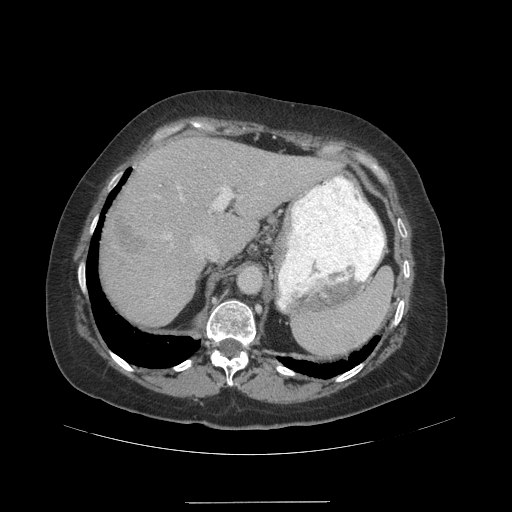
Contrast-enhanced abdominal CT (liver protocol), one axial slice; slice 72 of 99 in the series (ordered by position); reconstruction kernel STANDARD; soft-tissue window (W 400 / L 40 HU); 2.5 mm slice thickness; 512 × 512 image matrix, field of view 440 × 440 mm. Case-level facts recorded for this patient, not image findings: diagnosis: hepatocellular carcinoma (patient treated with transarterial chemoembolisation; whether this scan precedes or follows treatment is not stated here); TNM stage (as recorded): Stage-IVA; Child-Pugh class: A.
Annotated regions visible in this slice (semi-automatically segmented with operator editing):
- abdominal aorta: box from (x=237, y=265) to (x=262, y=293) px
- liver parenchyma outside the tumour (the mass and vessels are separate outlines, so this box may not span the whole liver): (x=102, y=136)–(x=339, y=324)
- mass: (x=109, y=214)–(x=147, y=260)
- liver vessels: (x=165, y=183)–(x=263, y=253)